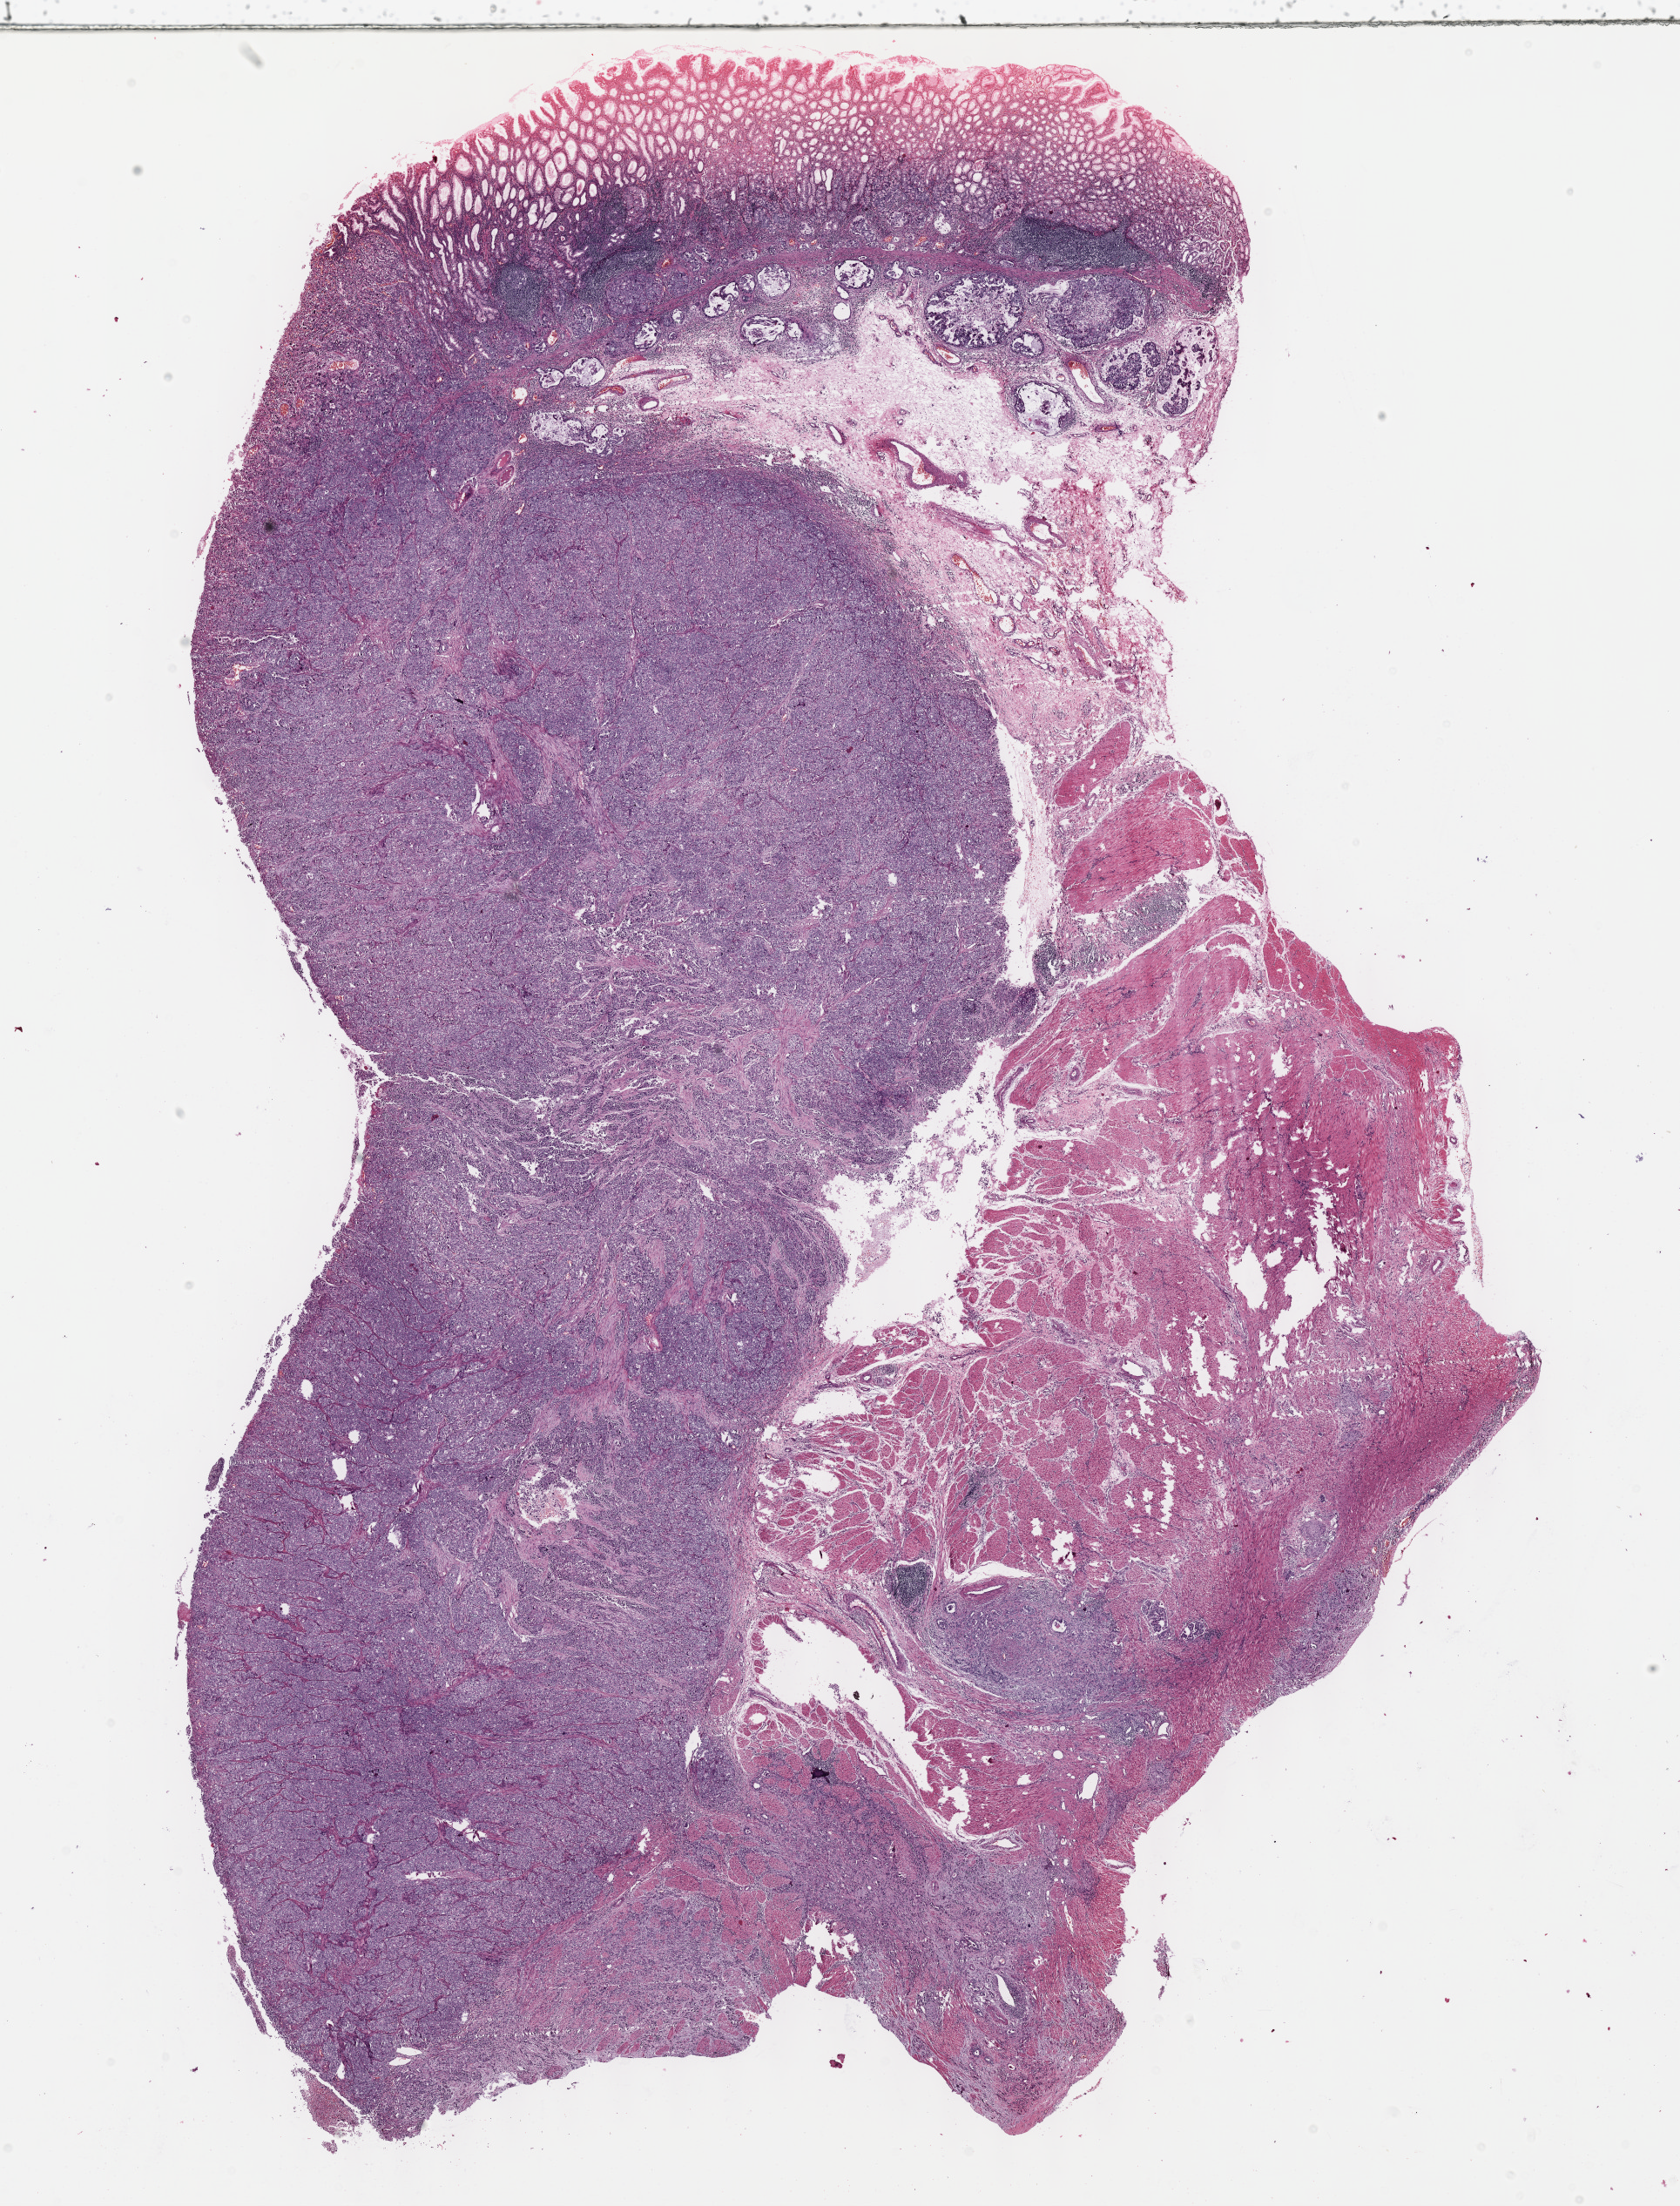
H&E whole-slide image — whole scanned area (about 15.6 x 20.5 mm) shown as a low-resolution overview; formalin-fixed paraffin-embedded (FFPE) diagnostic section; primary tumour sample from the stomach. Female, age 61 years at initial diagnosis. Histologic grade: G3 (poorly differentiated).
Diagnosis: Adenocarcinoma, intestinal type. AJCC pathologic stage: II (6th edition).